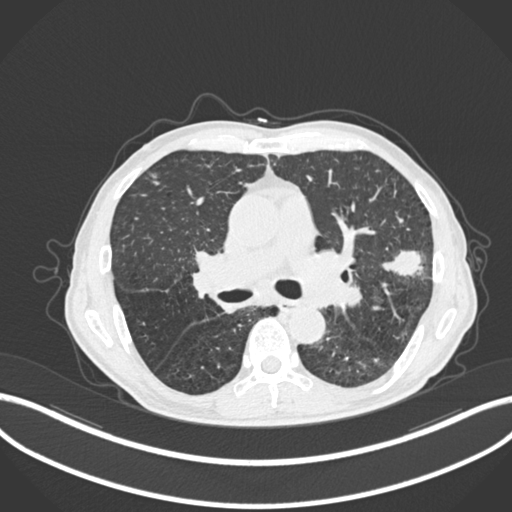
Chest CT, one axial slice; slice 146 of 287 in the series (ordered by position); 120 kVp; lung window (W 1500 / L -600 HU); 512 × 512 image matrix, field of view 400 × 400 mm. Male patient, age 74 years. Case-level facts recorded for this patient, not image findings: clinical TNM (as recorded): T2a N1 M0.
Annotated regions visible in this slice (rectangle marked by the reading radiologist):
- lung tumour (recorded histology: adenocarcinoma): bounding box [x1, y1, x2, y2] px = [376, 246, 430, 283]